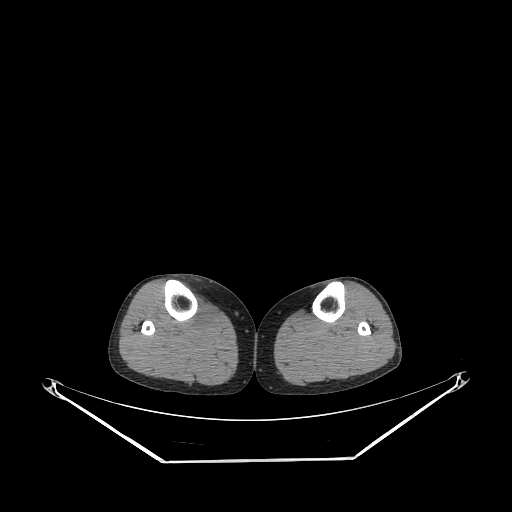
CT of an extremity soft-tissue mass (from a PET/CT study), one axial slice; position 149 of 267 along the scan axis; reconstruction kernel STANDARD; 140 kVp; soft-tissue window (W 400 / L 40 HU); 3.75 mm slice thickness; 512 × 512 image matrix, field of view 500 × 500 mm. Female patient. From the clinical record (not read from this slice): histological type: undifferentiated – high grade; grade: high; site of the primary tumour: right thigh.
Outlined on this slice (expert contour drawn on MRI and transferred to this co-registered scan by the dataset authors):
- gross tumour volume (mass): bounding box <190,297,218,330> (left, top, right, bottom; pixels)